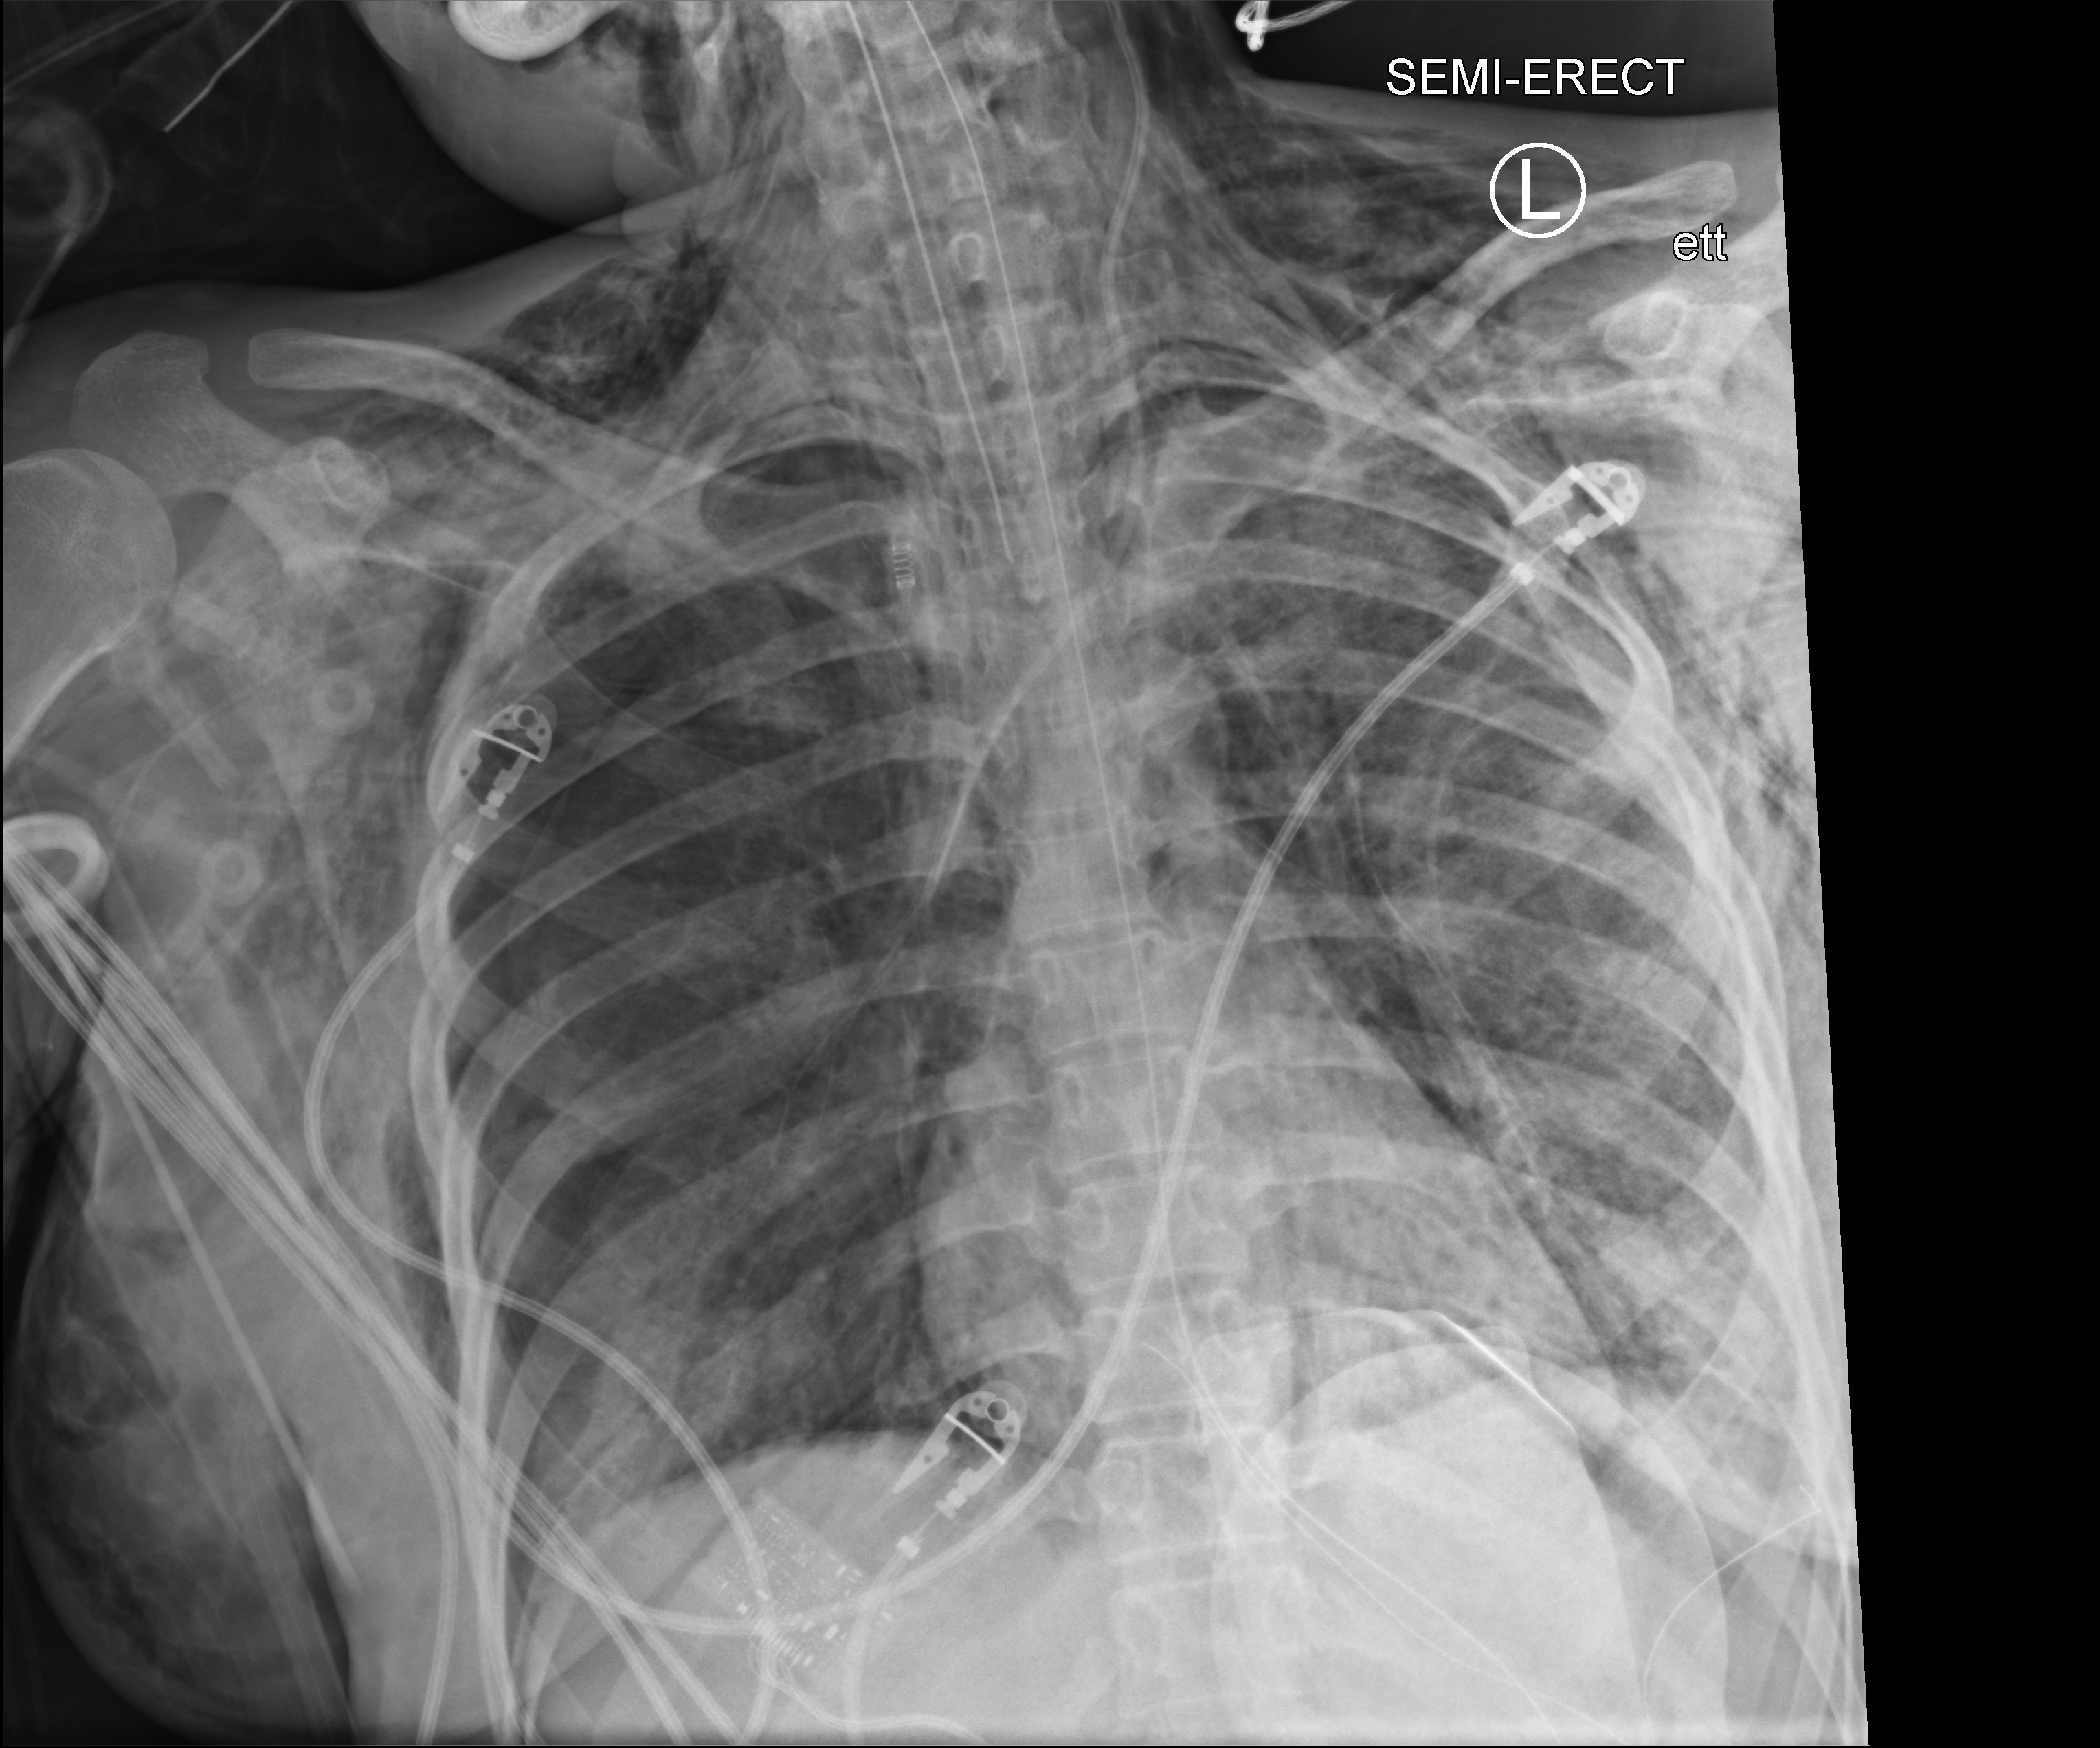
Bedside chest radiograph (computed radiography), anteroposterior (AP) projection. Adult patient hospitalised with COVID-19, age 18–59 years.
From the hospital-stay record, not from the radiograph (when in the stay this image was taken is not recorded): smoking status (admission record): never.